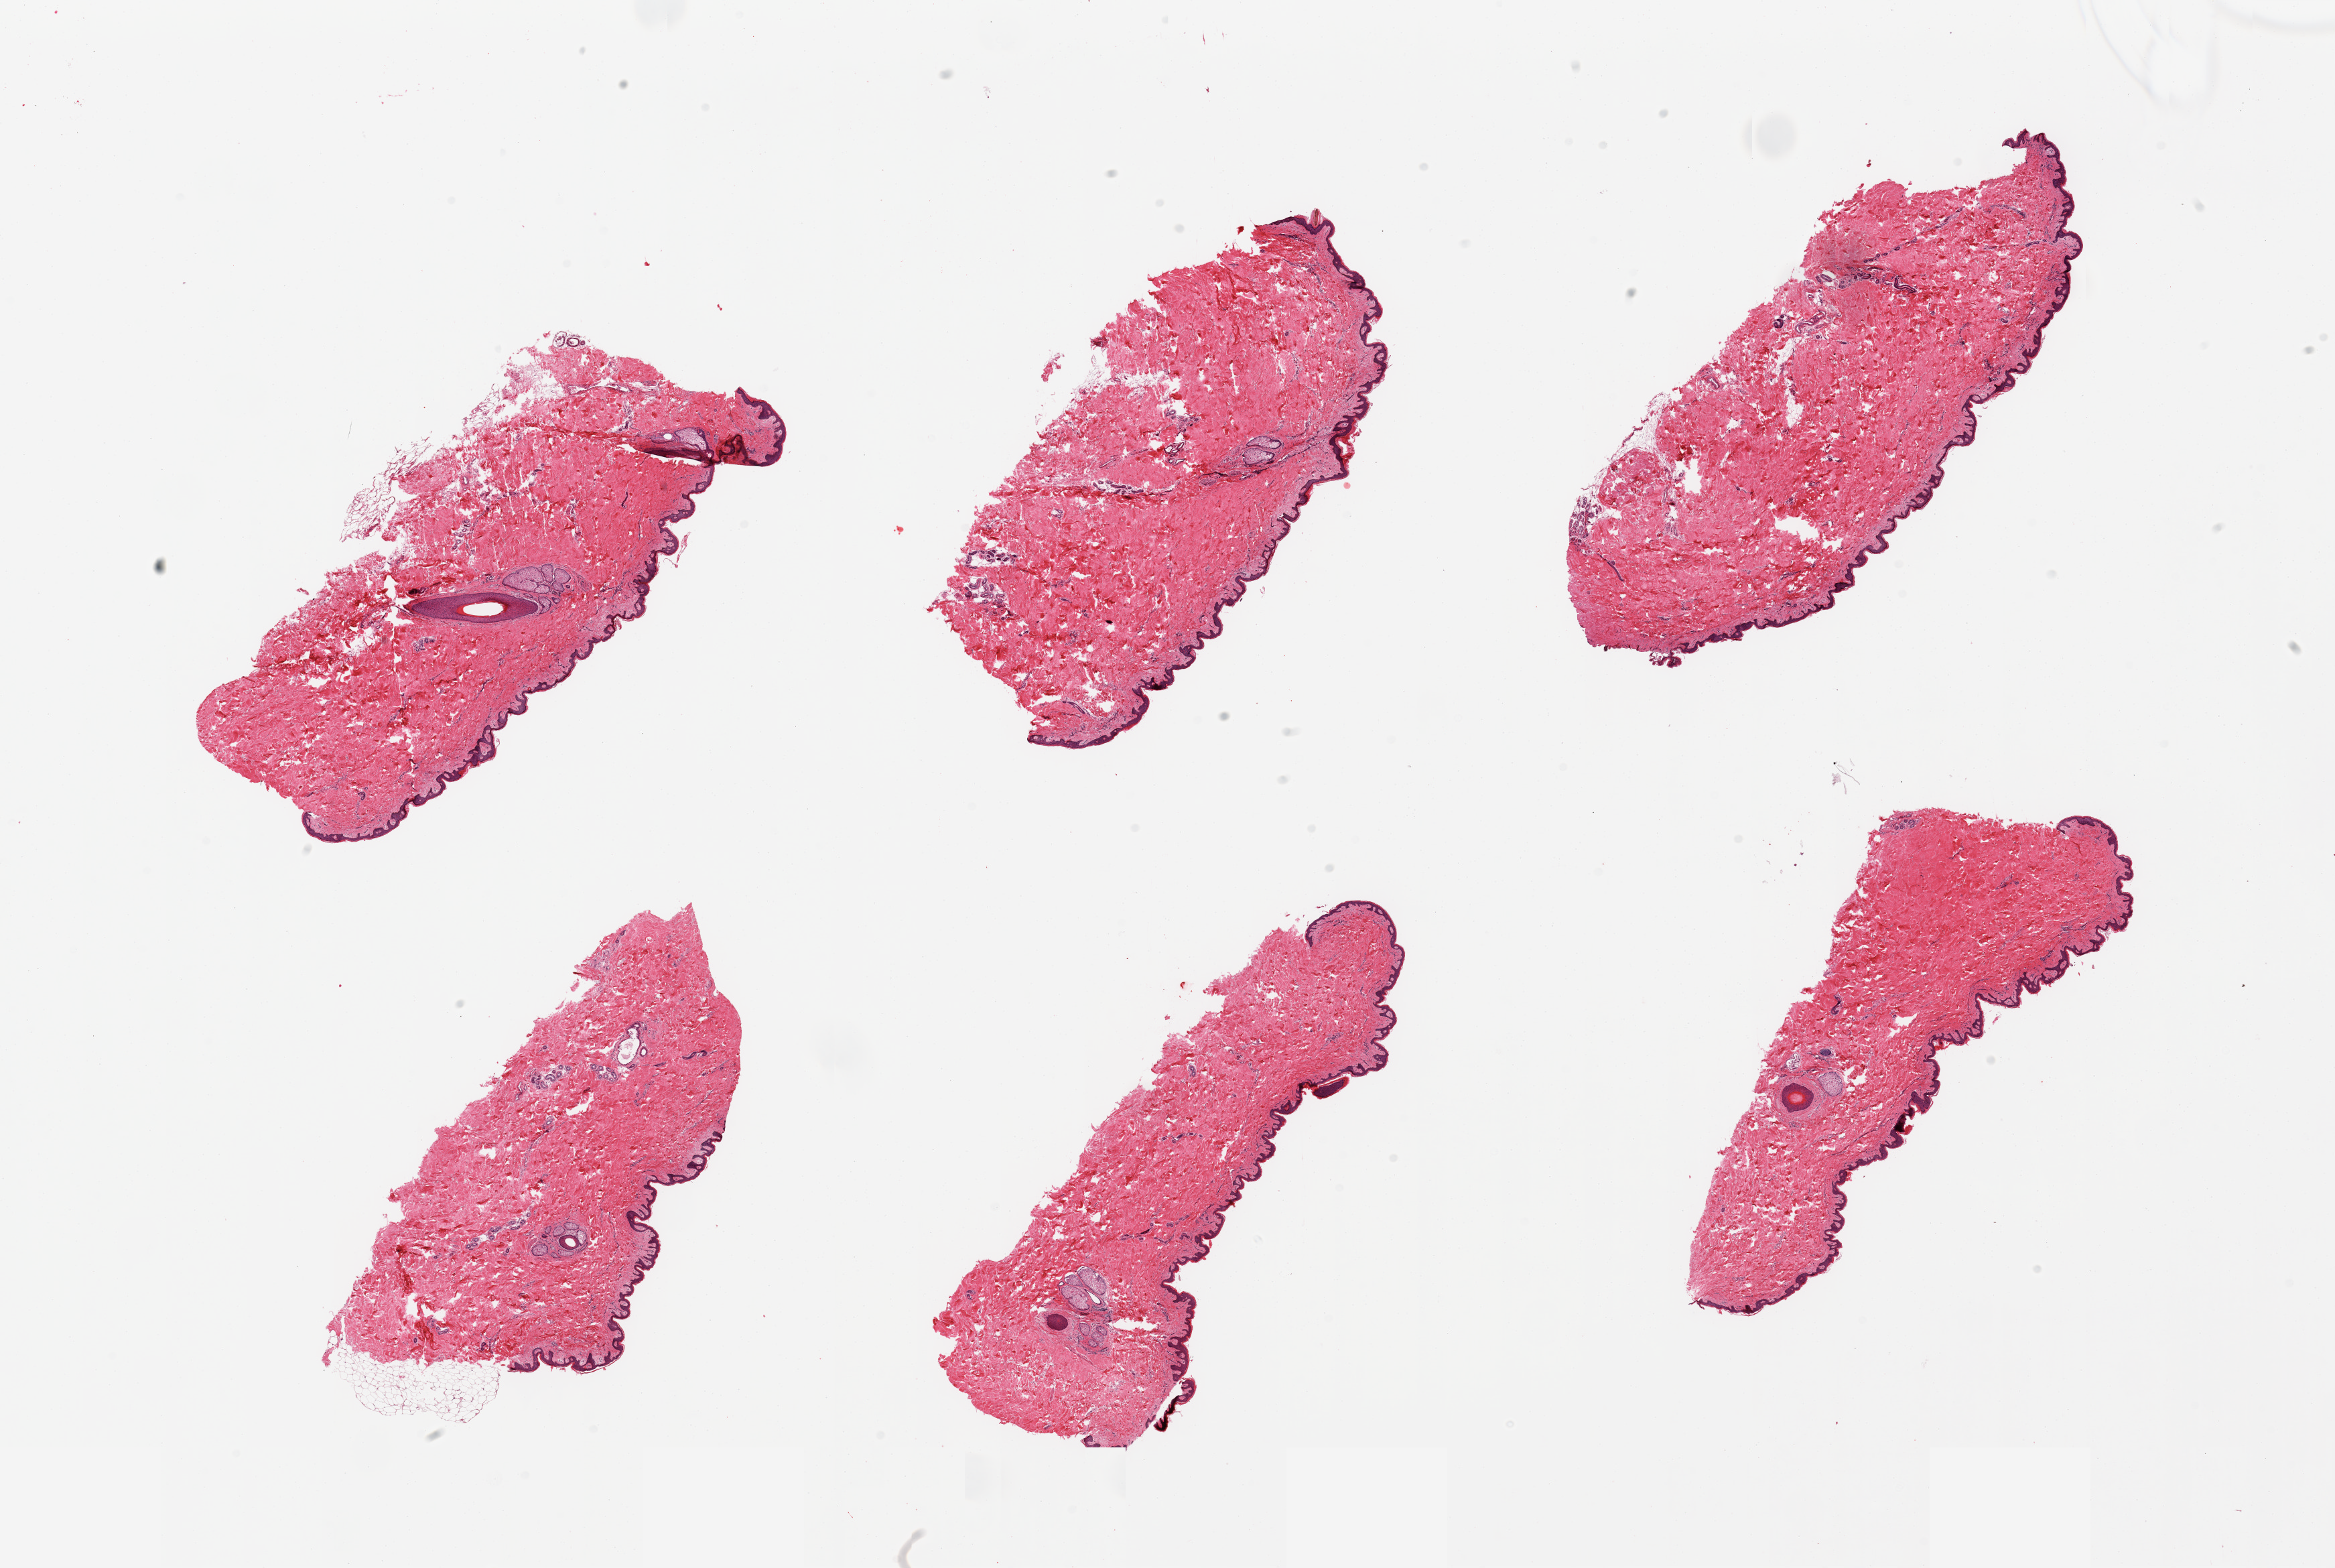
Digitized haematoxylin and eosin-stained section, whole scanned area (about 27.6 x 18.5 mm) shown as a low-resolution overview; PAXgene-fixed, paraffin-embedded tissue; sampled site (target tissue): skin of suprapubic region; donor tissue sample.
Review note (as recorded): 6 pieces, squamous epithelium is ~45-50 microns, no significant adherent fat.